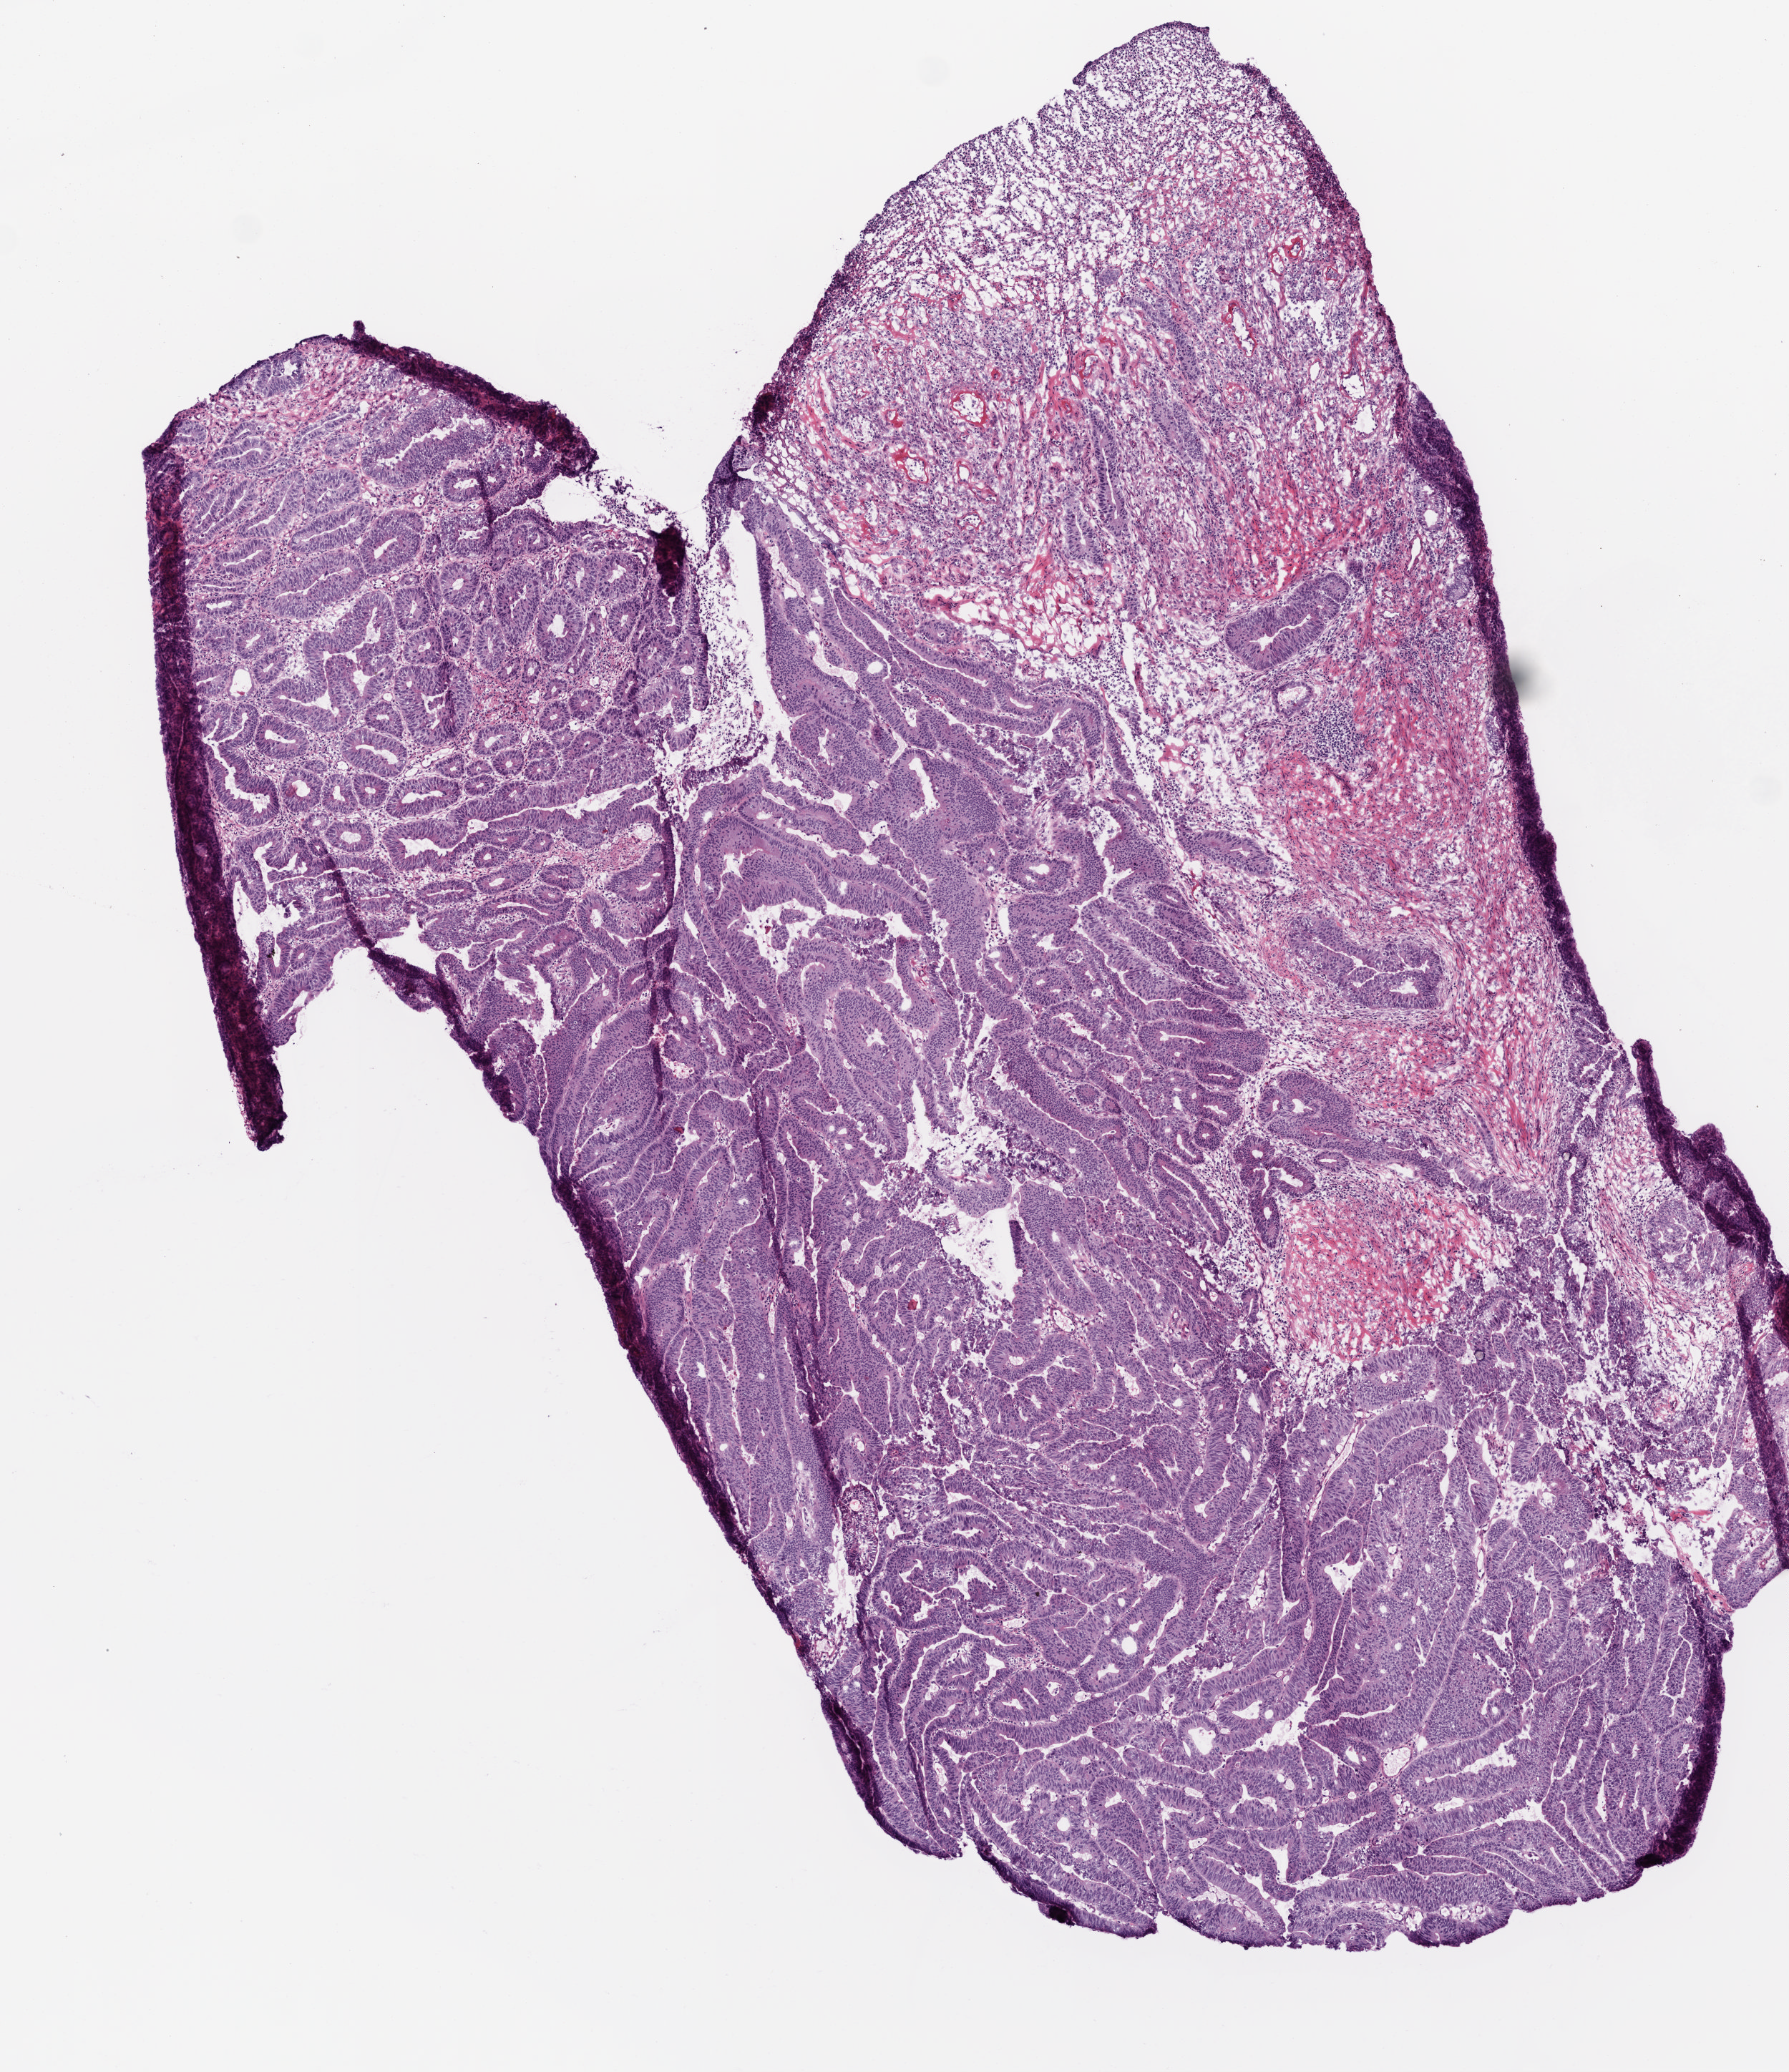
H&E-stained whole-slide image — low-resolution overview of the scanned area, about 5.0 x 5.8 mm (slide scanned at 20x), frozen section from the top of the tissue portion, sample: primary tumour, colon. Female patient; age at initial diagnosis 36 years. Slide review estimates, as recorded: tumour cells 100%, tumour nuclei 70%, normal cells 0%, stromal cells 0%, necrosis 0%.
TNM: T2 N0 M0. AJCC pathologic stage: I (5th edition). Diagnosis: Adenocarcinoma, NOS. Lymph nodes positive (case pathology): 0 of 22 examined.